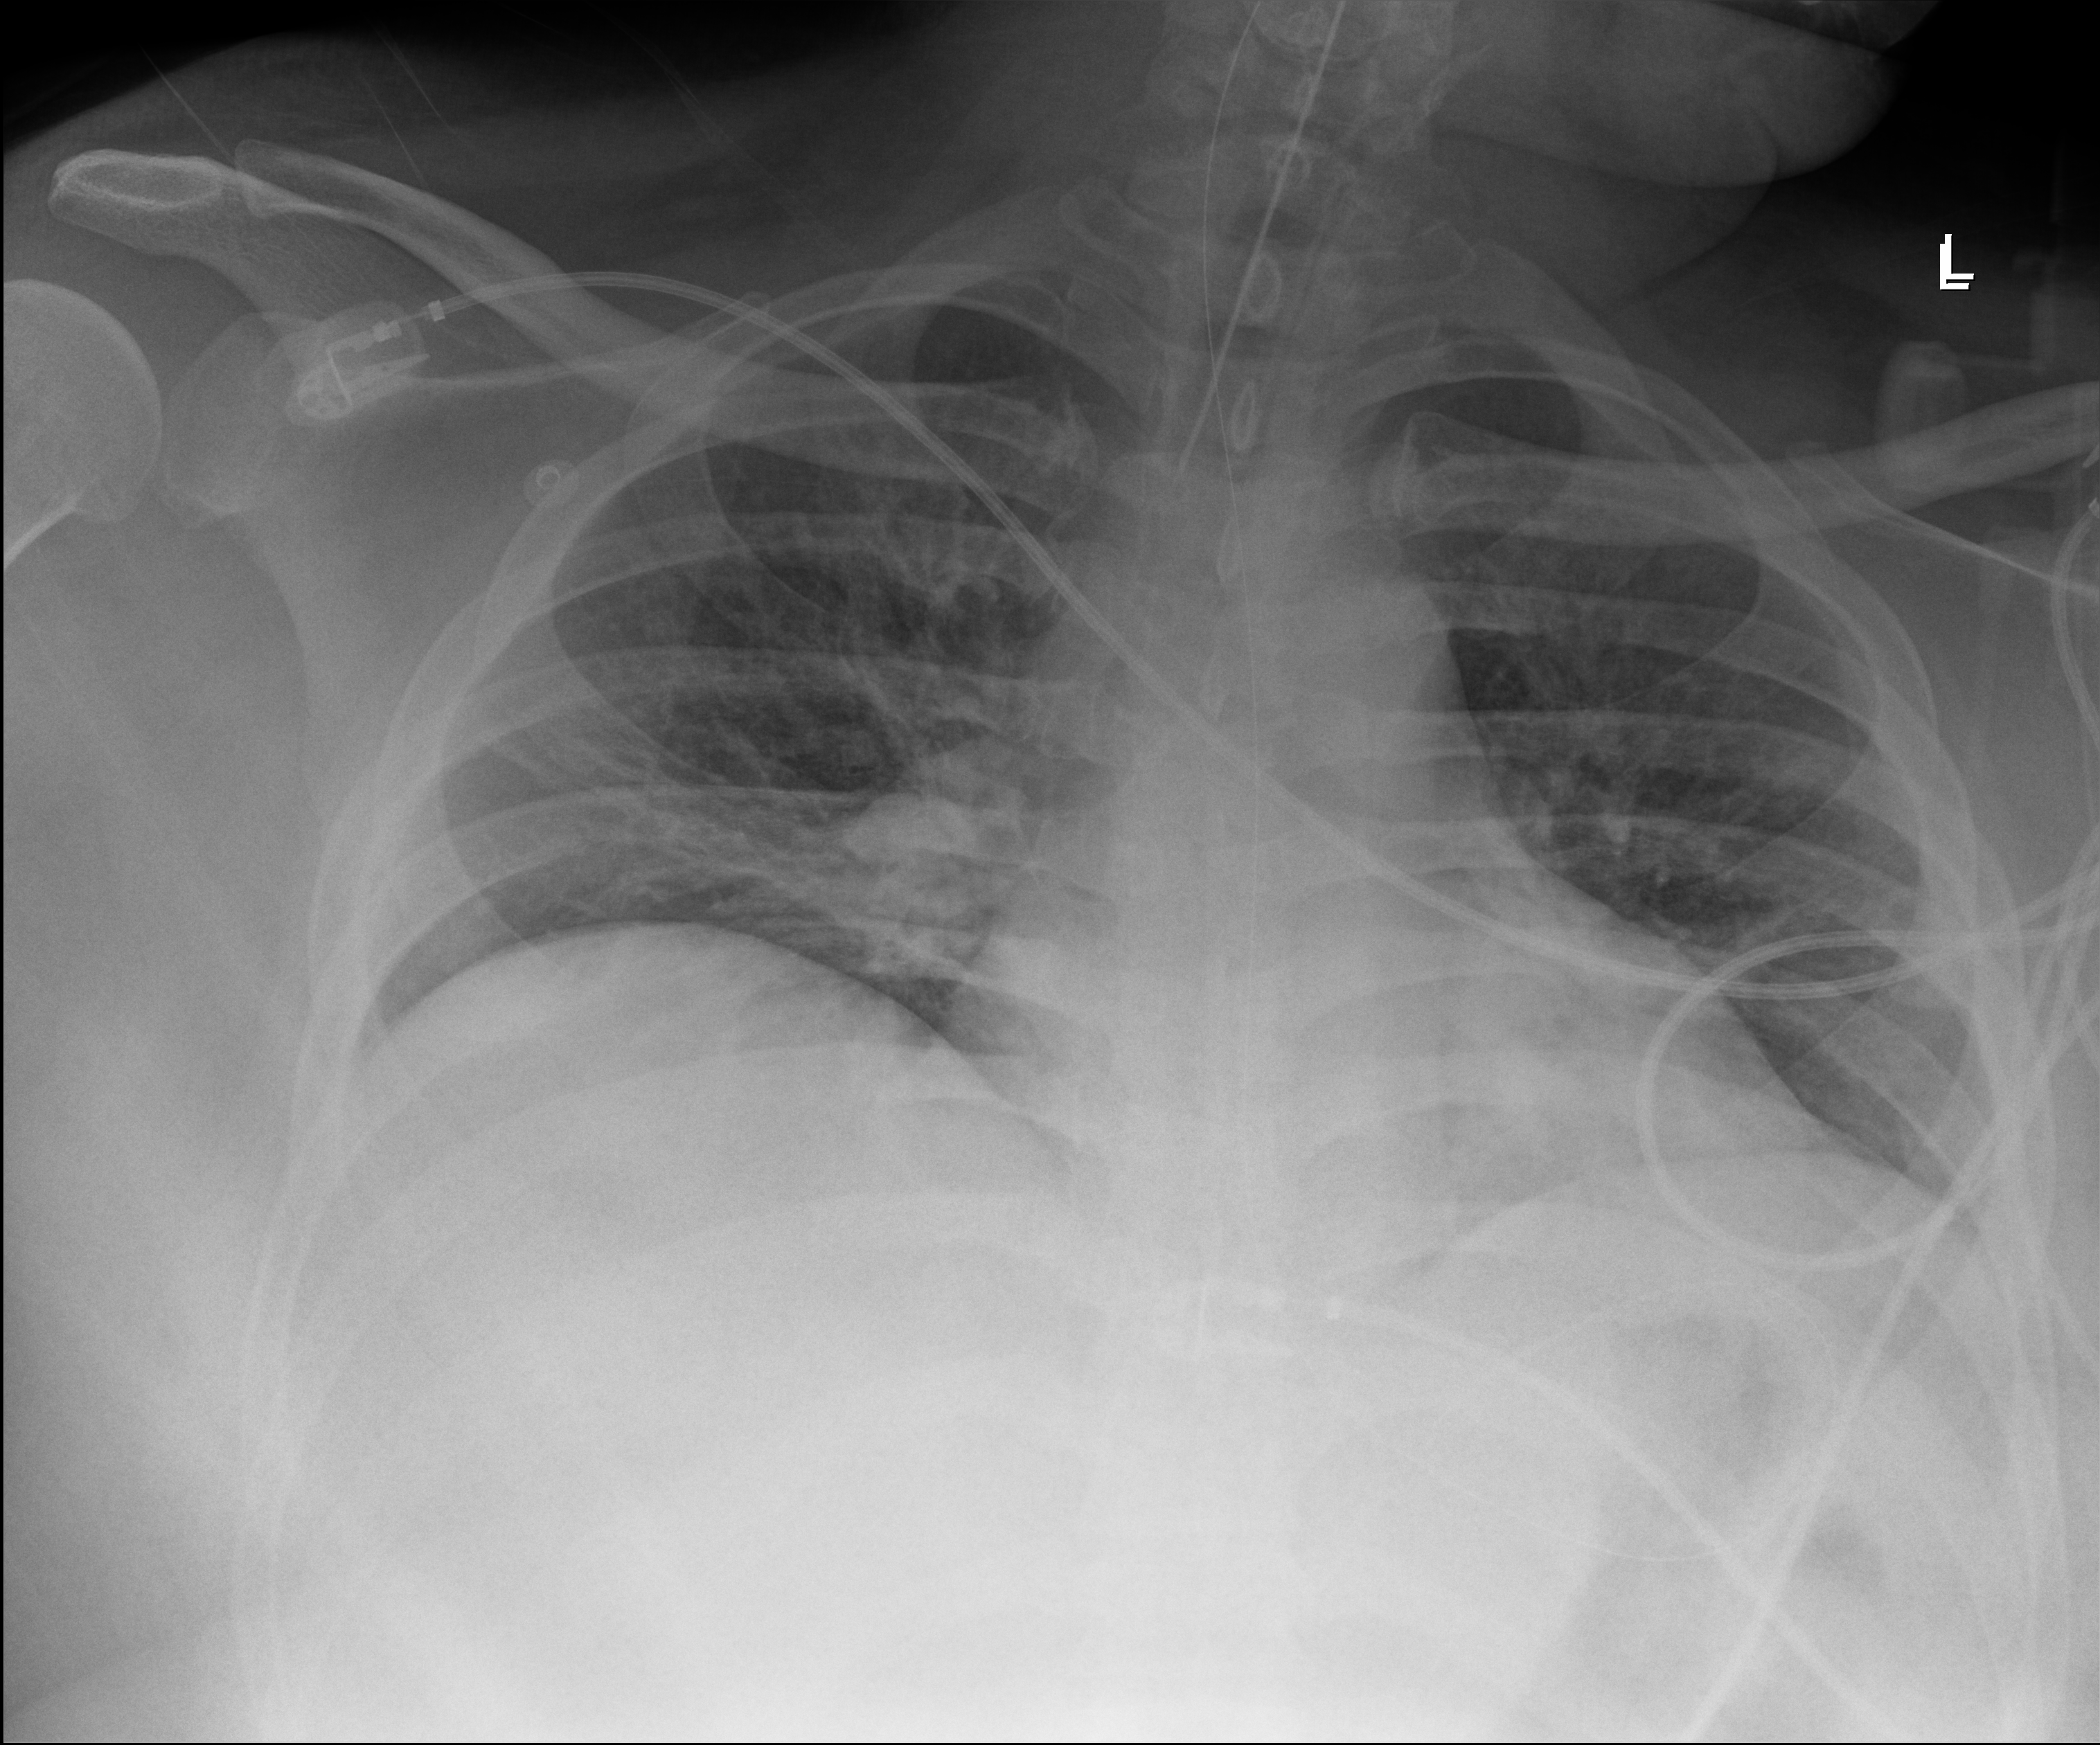
Chest X-ray (portable); anteroposterior (AP) projection. Male patient hospitalised with COVID-19, age 18–59 years.
Hospital-stay facts (about this admission, not read from this image; timing relative to this image not recorded):
- admitted to intensive care during this hospital stay: yes